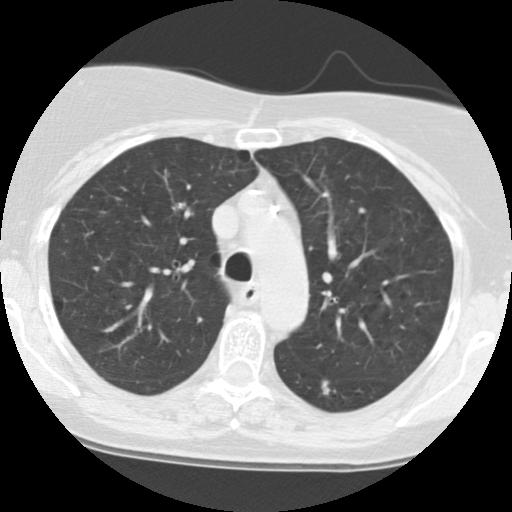
Low-dose screening chest CT, axial slice; baseline annual screen; lung window (W 1500 / L -600 HU); standard (soft-tissue) reconstruction kernel (STANDARD); 120 kVp. Female participant, aged 63 years at enrolment.
Lesion marked by an expert reader, bounding box <304,372,347,409> (left, top, right, bottom; pixels). The screening reader recorded 2 non-calcified nodules or masses ≥4 mm on this exam; which of them this box marks is not recorded. Official screen result: positive, change unspecified: nodule(s) >= 4 mm or enlarging nodule(s), mass(es), or other non-specific abnormalities suspicious for lung cancer.